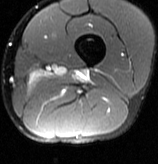
MRI of an extremity soft-tissue mass, one axial slice. Slice 15 of 70 in the series (ordered by position). T2-weighted fat-saturated. MR volume resampled by the dataset authors to the PET/CT grid (not the native acquisition matrix). 158 × 164 image matrix, field of view 154 × 160 mm. Male patient. From the clinical record (not read from this slice): histological type: extraskeletal osteosarcoma; grade: high; site of the primary tumour: left adductur.
Outlined on this slice (expert contour drawn on MRI and transferred to this co-registered scan by the dataset authors):
- gross tumour volume (mass): bounding box <72,69,89,81> (left, top, right, bottom; pixels)